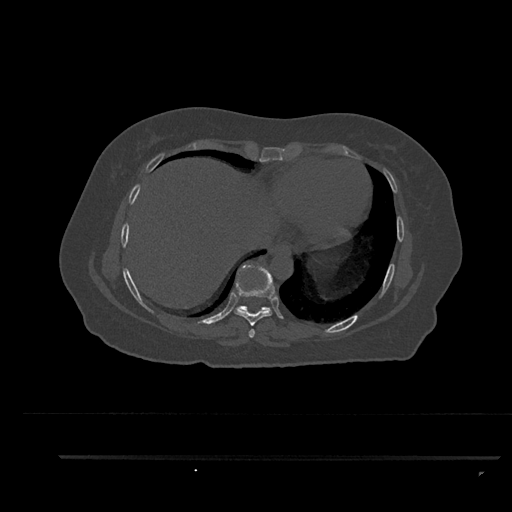
CT including the spine, one axial slice. Position 448 of 797 along the scan axis. Reconstruction kernel Br40s/3. 120 kVp. Bone window (W 1800 / L 400 HU). 0.5 mm slice thickness. 512 × 512 image matrix, field of view 408 × 408 mm. Female patient, age 44 years. From the clinical record (not read from this slice): primary cancer: renal; vertebrae with lytic lesions (as recorded): L1.
Outlined on this slice (semi-automatic segmentation, software-assisted and operator-edited):
- T7 vertebra: box from (x=248, y=329) to (x=255, y=338) px
- T8 vertebra: (x=234, y=266)–(x=275, y=326)
- T9 vertebra: (x=235, y=306)–(x=271, y=313)